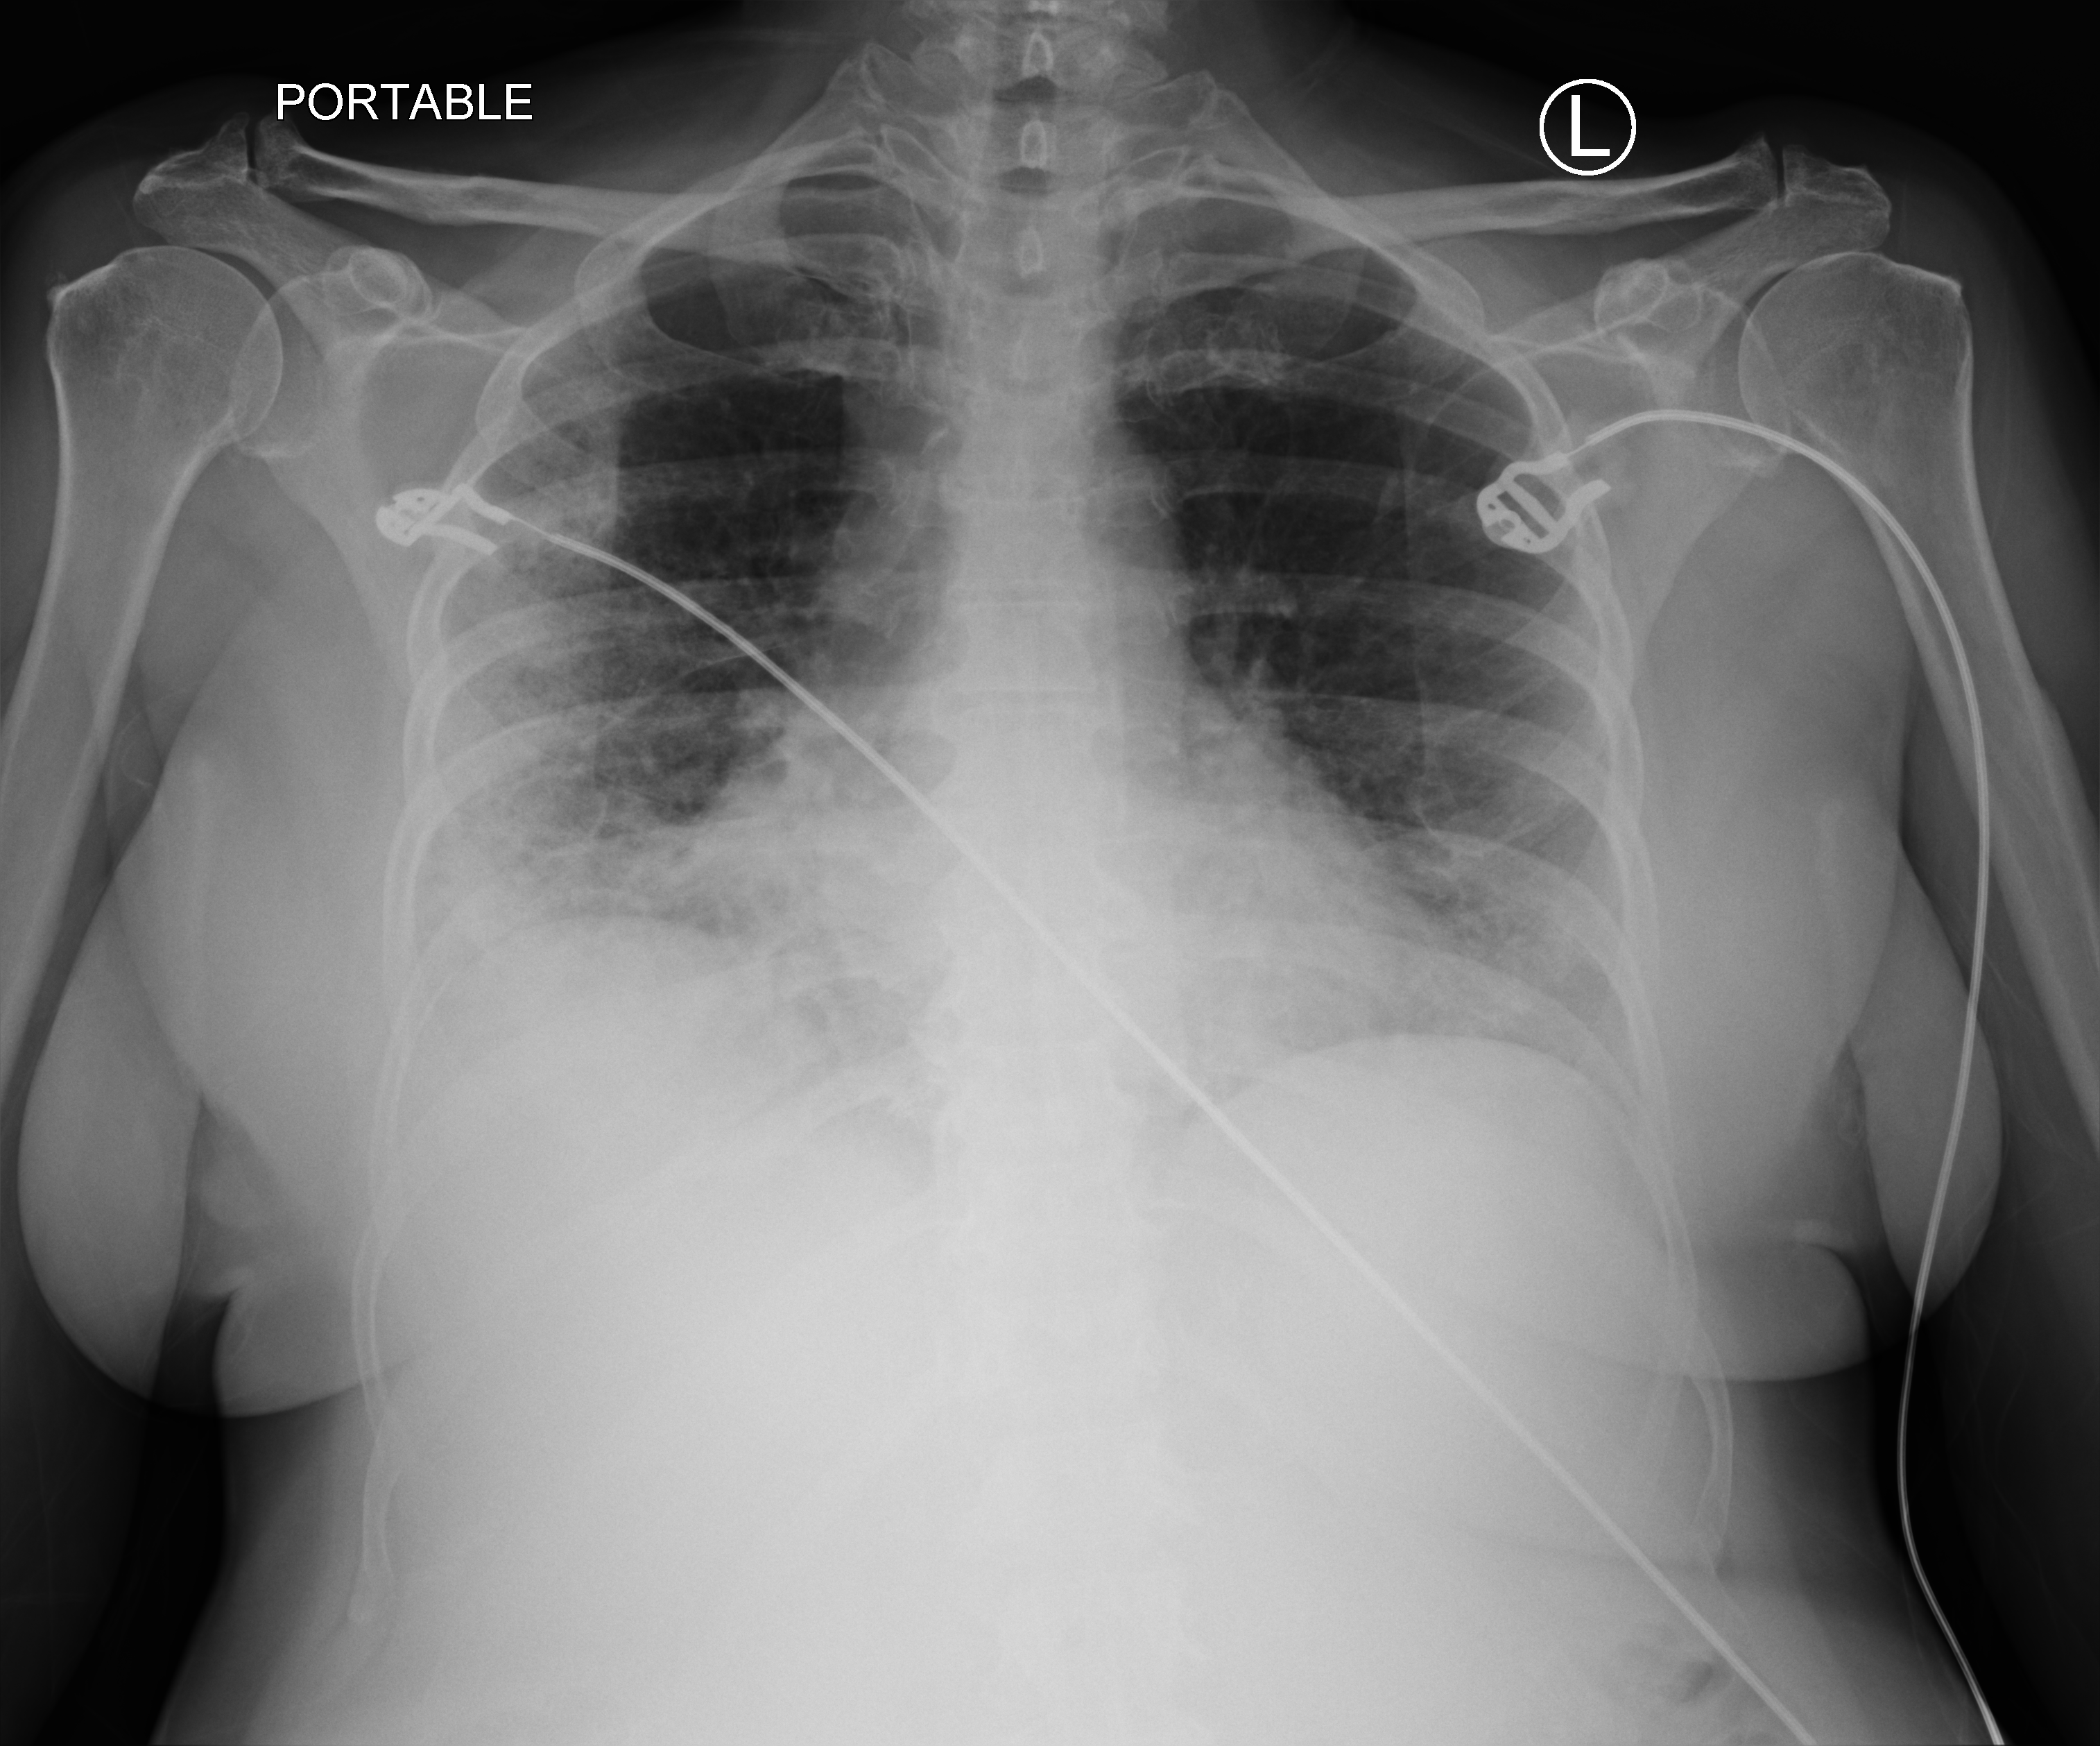
Bedside chest radiograph (computed radiography); anteroposterior (AP) projection. Female patient hospitalised with COVID-19, age 60–74 years.
From the hospital-stay record, not from the radiograph (when in the stay this image was taken is not recorded): length of hospital stay: 10 days; admitted to intensive care during this hospital stay: no.